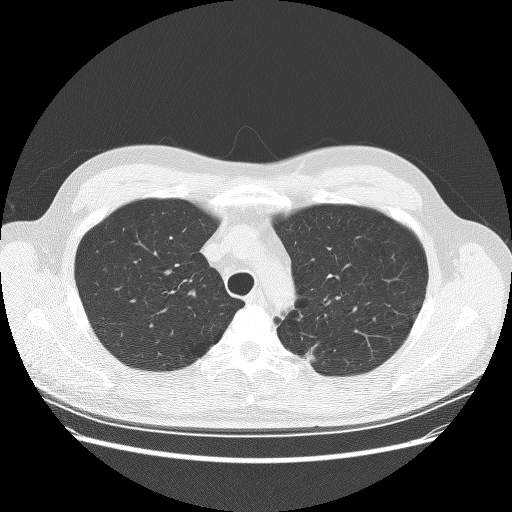
Low-dose screening chest CT, one axial slice. Position 205 of 253 along the scan axis. Lung window (W 1500 / L -600 HU). 2.5 mm slice thickness. 512 × 512 image matrix, field of view 370 × 370 mm.
Outlined on this slice (manually delineated by an expert):
- lesion 2 (nodule): bounding box [x1, y1, x2, y2] px = [306, 350, 315, 362]